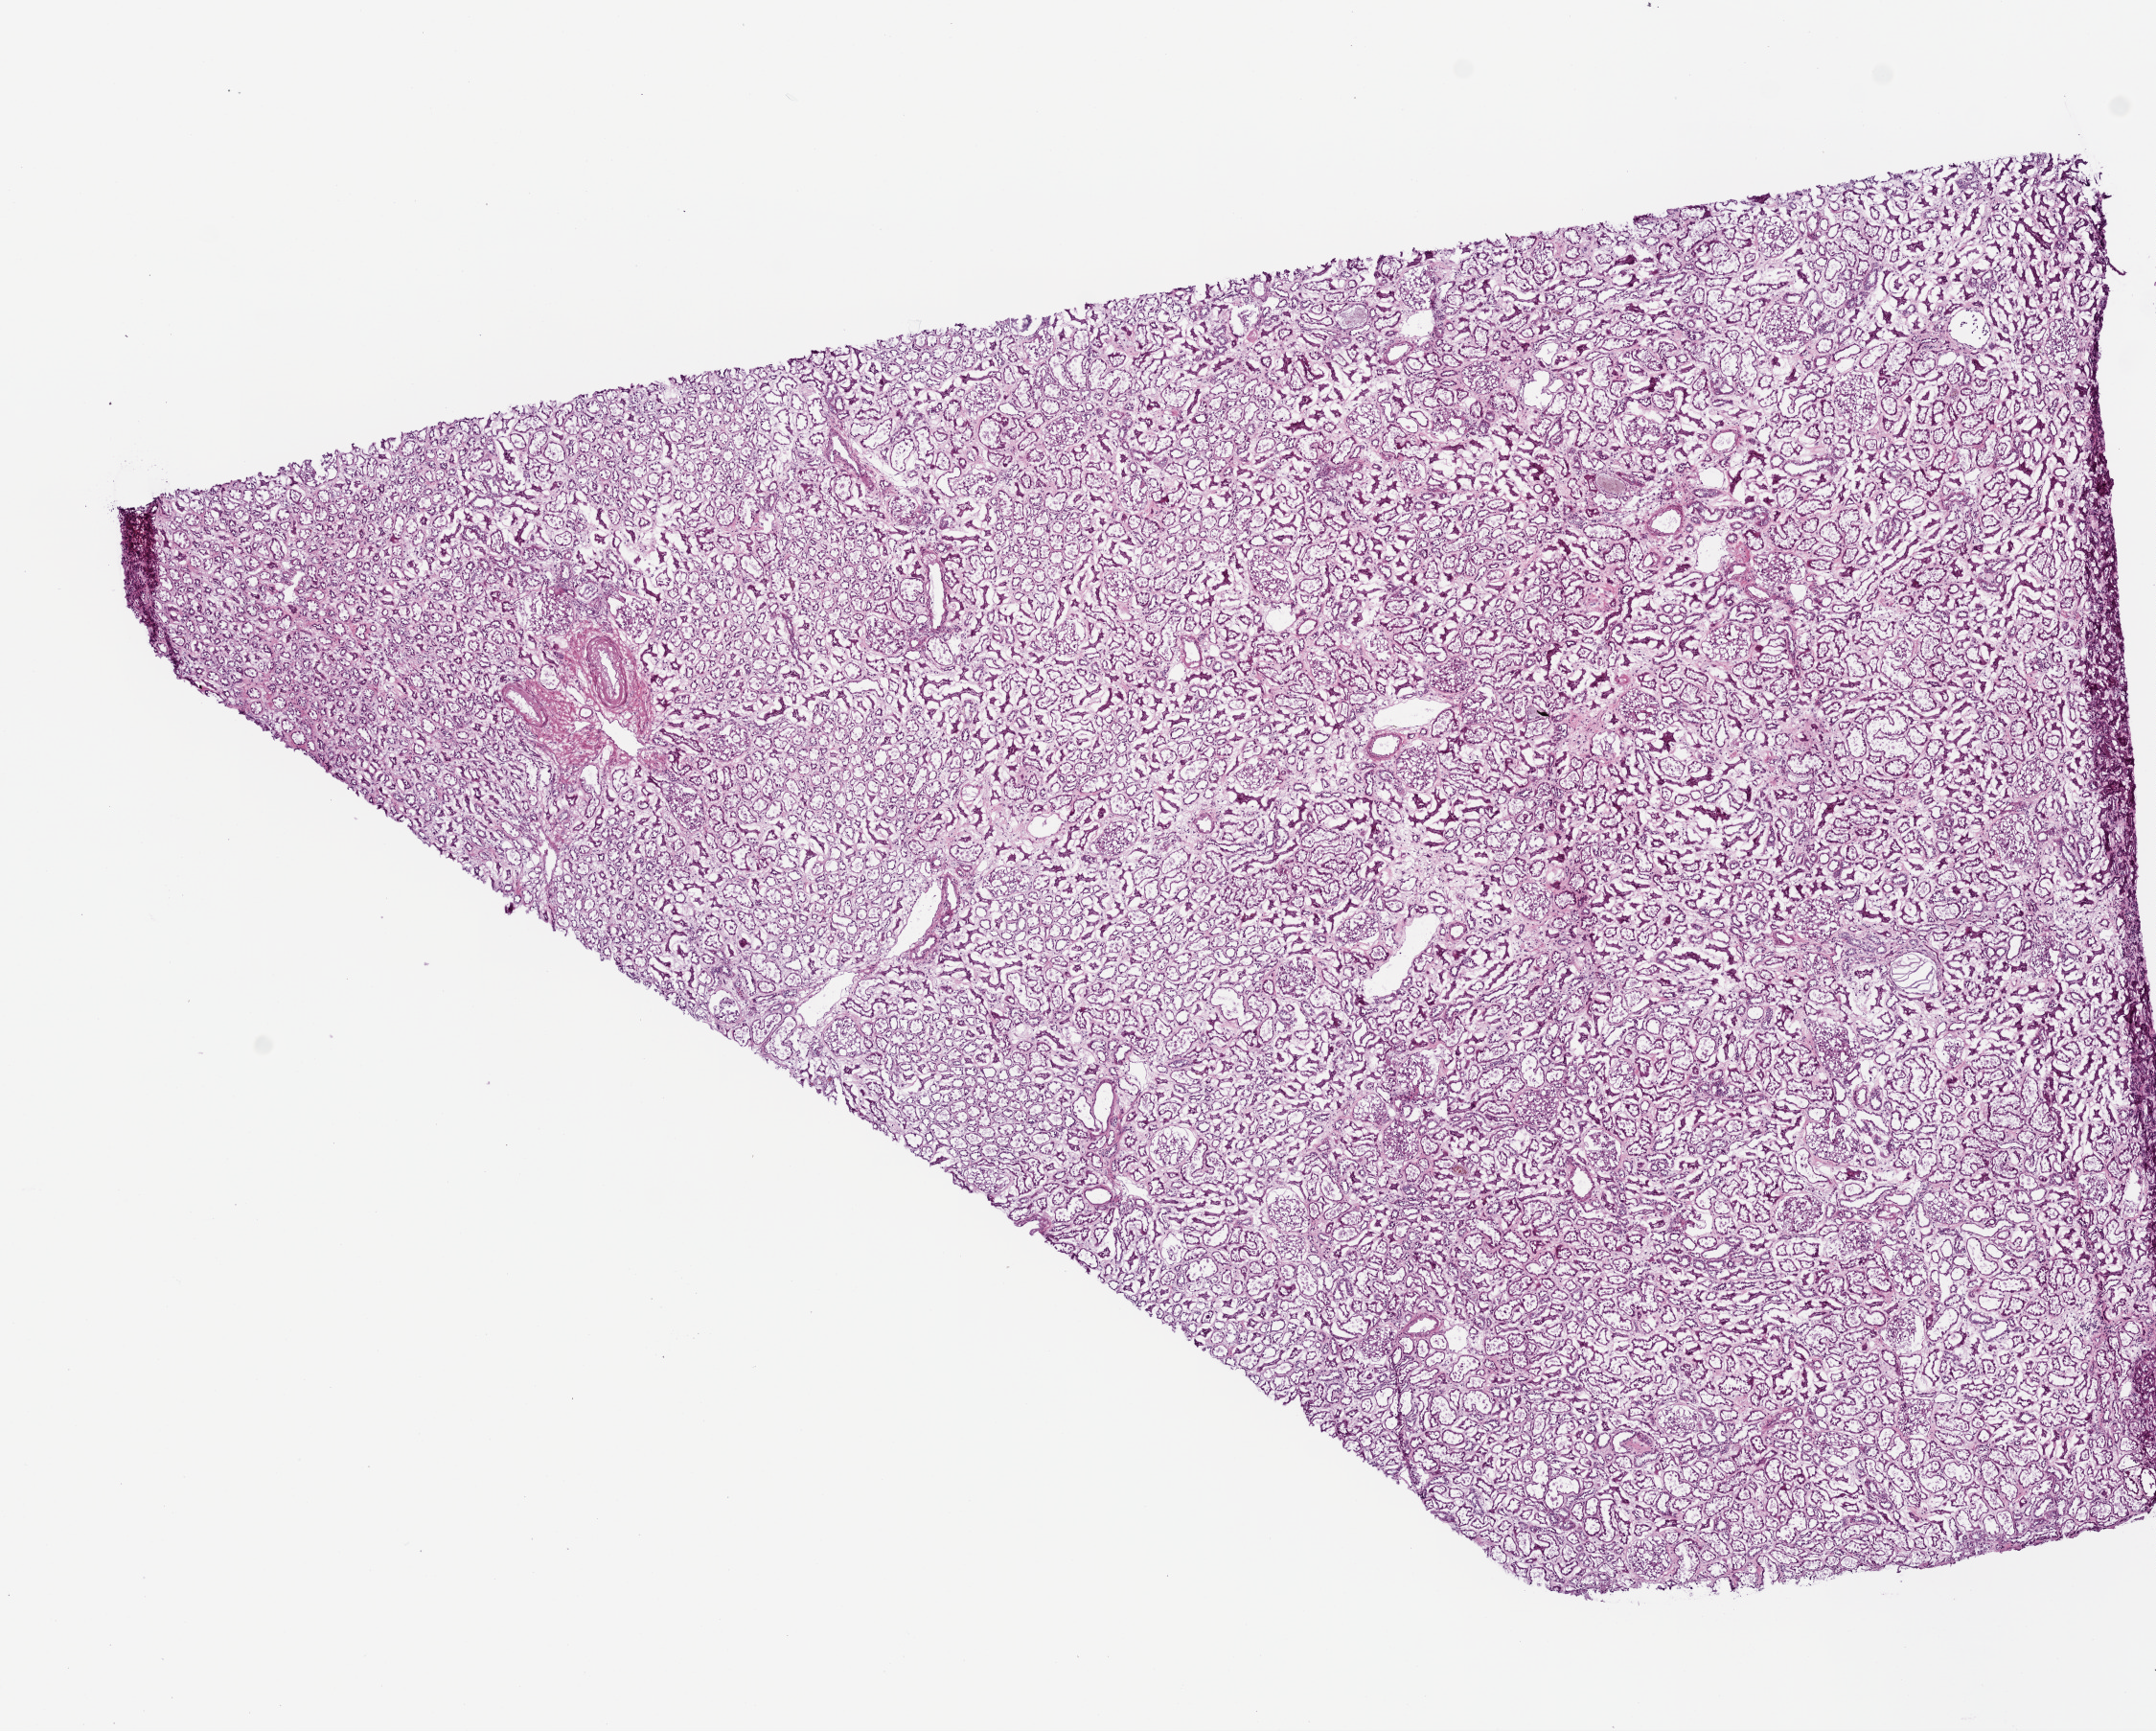
Whole-slide histology image, H&E-stained, whole scanned area (about 9.0 x 7.2 mm) shown as a low-resolution overview; frozen section from the top of the tissue portion; solid tissue normal (non-tumour tissue) sample from the kidney. Patient: female, age at initial diagnosis 62 years.
This section: solid tissue normal (non-tumour) sample from the same patient. Patient diagnosis: Clear cell adenocarcinoma, NOS.